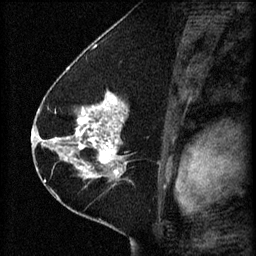
Breast MRI (dynamic contrast-enhanced), one sagittal slice; position 33 of 60 along the scan axis; 3 images stored at this slice position (order not interpretable as contrast timing); 1.5 T; TE 4.2 ms, TR 8.2 ms; 256 × 256 image matrix, field of view 180 × 180 mm. Patient: female, 41 years.
Outlined on this slice (semi-automatically segmented with operator editing):
- analysis volume of interest (the breast-tissue region the enhancement analysis was run in; not a lesion): bounding box (x1, y1, x2, y2) in pixels: (67, 92, 165, 173)
- tumour enhancement mask (voxels above the 70 % enhancement threshold inside the analysis volume of interest): (67, 92, 126, 173)